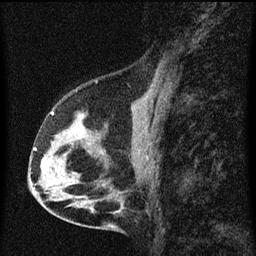
Breast MRI (dynamic contrast-enhanced), one sagittal slice. Slice 34 of 60 in the series (ordered by position). Dynamic contrast-enhanced series, image 2 of 3 at this slice position (ordered by acquisition). 1.5 T. TE 4.2 ms, TR 8 ms. 2 mm slice thickness. 256 × 256 image matrix, field of view 180 × 180 mm. Patient: female, 56 years.
Annotated regions visible in this slice (semi-automatic segmentation, software-assisted and operator-edited):
- analysis volume of interest (the breast-tissue region the enhancement analysis was run in; not a lesion): bounding box [x1, y1, x2, y2] px = [34, 114, 102, 181]
- tumour enhancement mask (voxels above the 70 % enhancement threshold inside the analysis volume of interest): [34, 148, 50, 171]